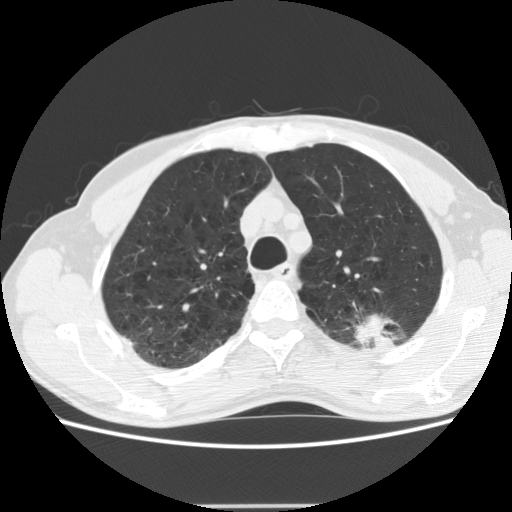
Low-dose screening chest CT, axial slice. Baseline annual screen. Lung window (W 1500 / L -600 HU). 2.5 mm slice thickness. Slice 41 of 191 in the series. 512 × 512 image matrix, field of view 352 × 352 mm. Male participant, aged 64 years at enrolment.
Expert reader's lesion annotation, bounding box [x1, y1, x2, y2] px = [341, 288, 429, 359]. Screening reader's record for this exam (one nodule recorded; not confirmed to be the boxed lesion): non-calcified nodule or mass ≥4 mm, left upper lobe, 27 × 19 mm, poorly defined margins, soft tissue attenuation. Official screen result: positive, change unspecified: nodule(s) >= 4 mm or enlarging nodule(s), mass(es), or other non-specific abnormalities suspicious for lung cancer. Participant outcome: lung cancer diagnosed 23 days after this screen — adenocarcinoma, NOS, left upper lobe, moderately differentiated (G2), stage IA (AJCC 6th edition), 29 mm at pathology.